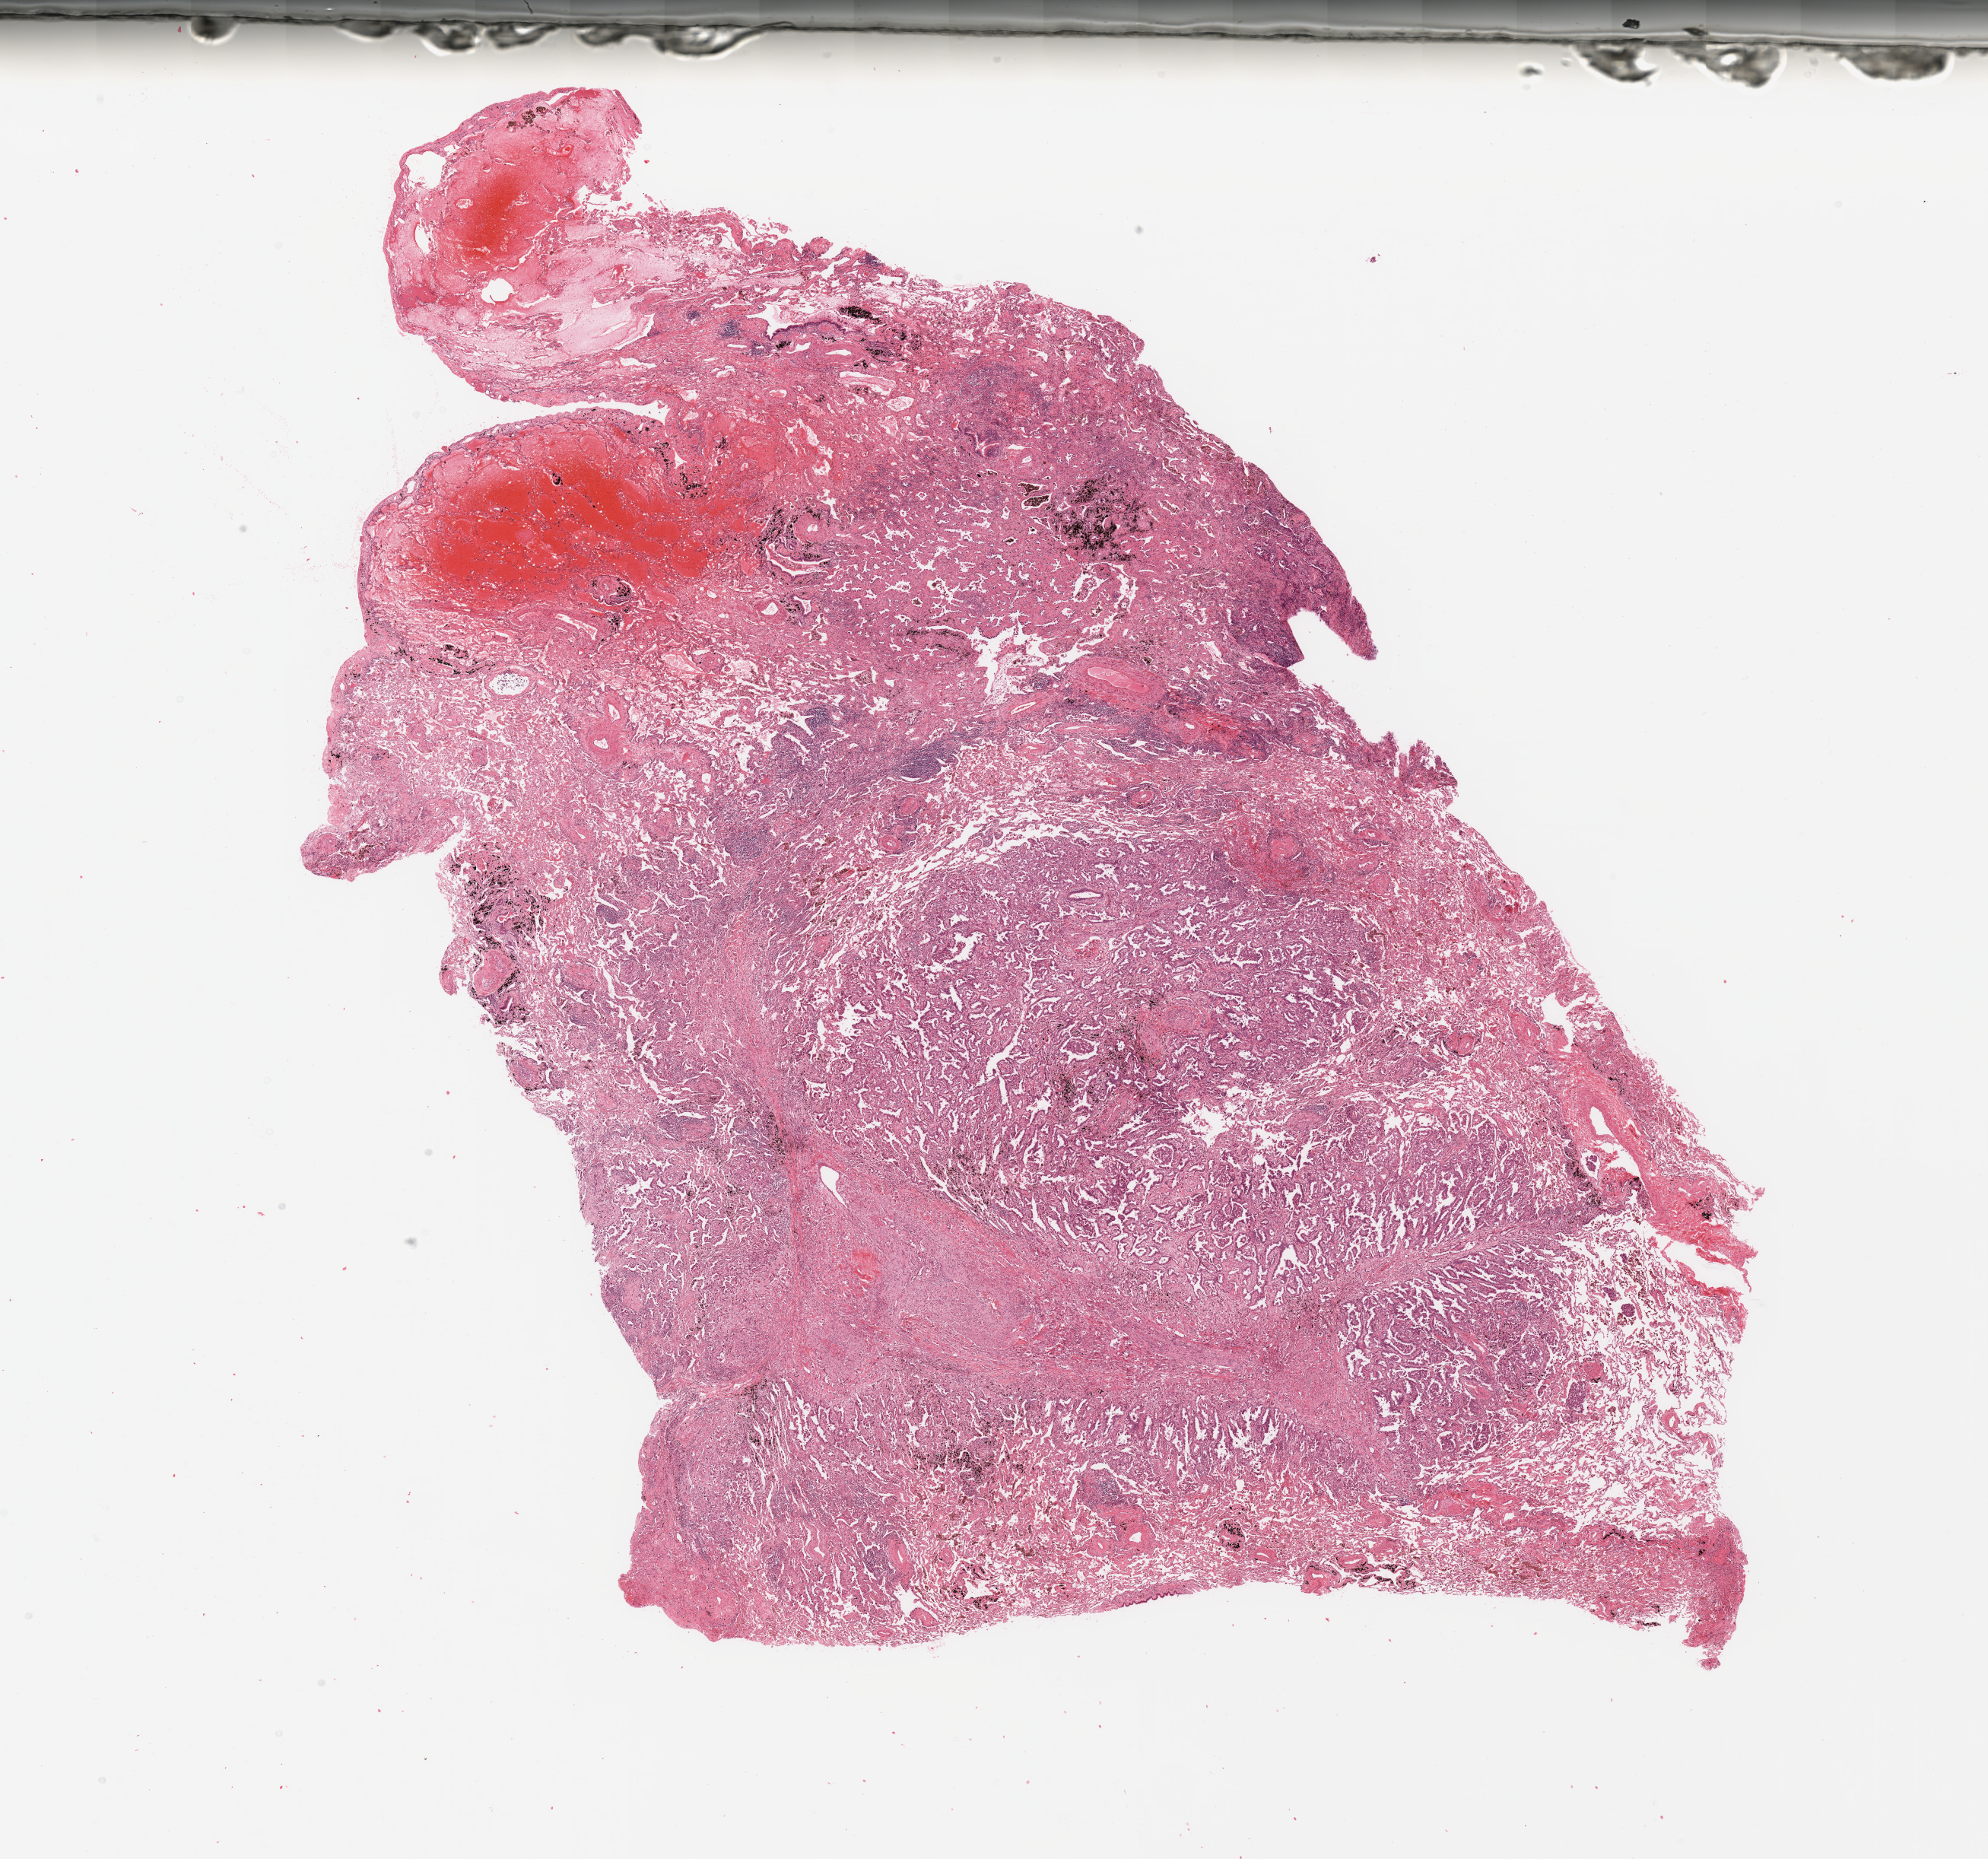
Digitized Hematoxylin and eosin (H&E) stained tissue section (whole slide) — shown as a low-resolution overview of the whole scanned area (about 20.7 x 19.3 mm, slide scanned at 20x). Tumour tissue sample, sampled site: lung. 59-year-old male patient. Histologic grade: G2 (moderately differentiated). Pathologist review of this section (percent, as recorded): tumour nuclei 70%, necrosis 5%.
* diagnosis: Adenocarcinoma, NOS
* primary tumour site (as recorded): right upper lobe
* AJCC pathologic stage: IIIA